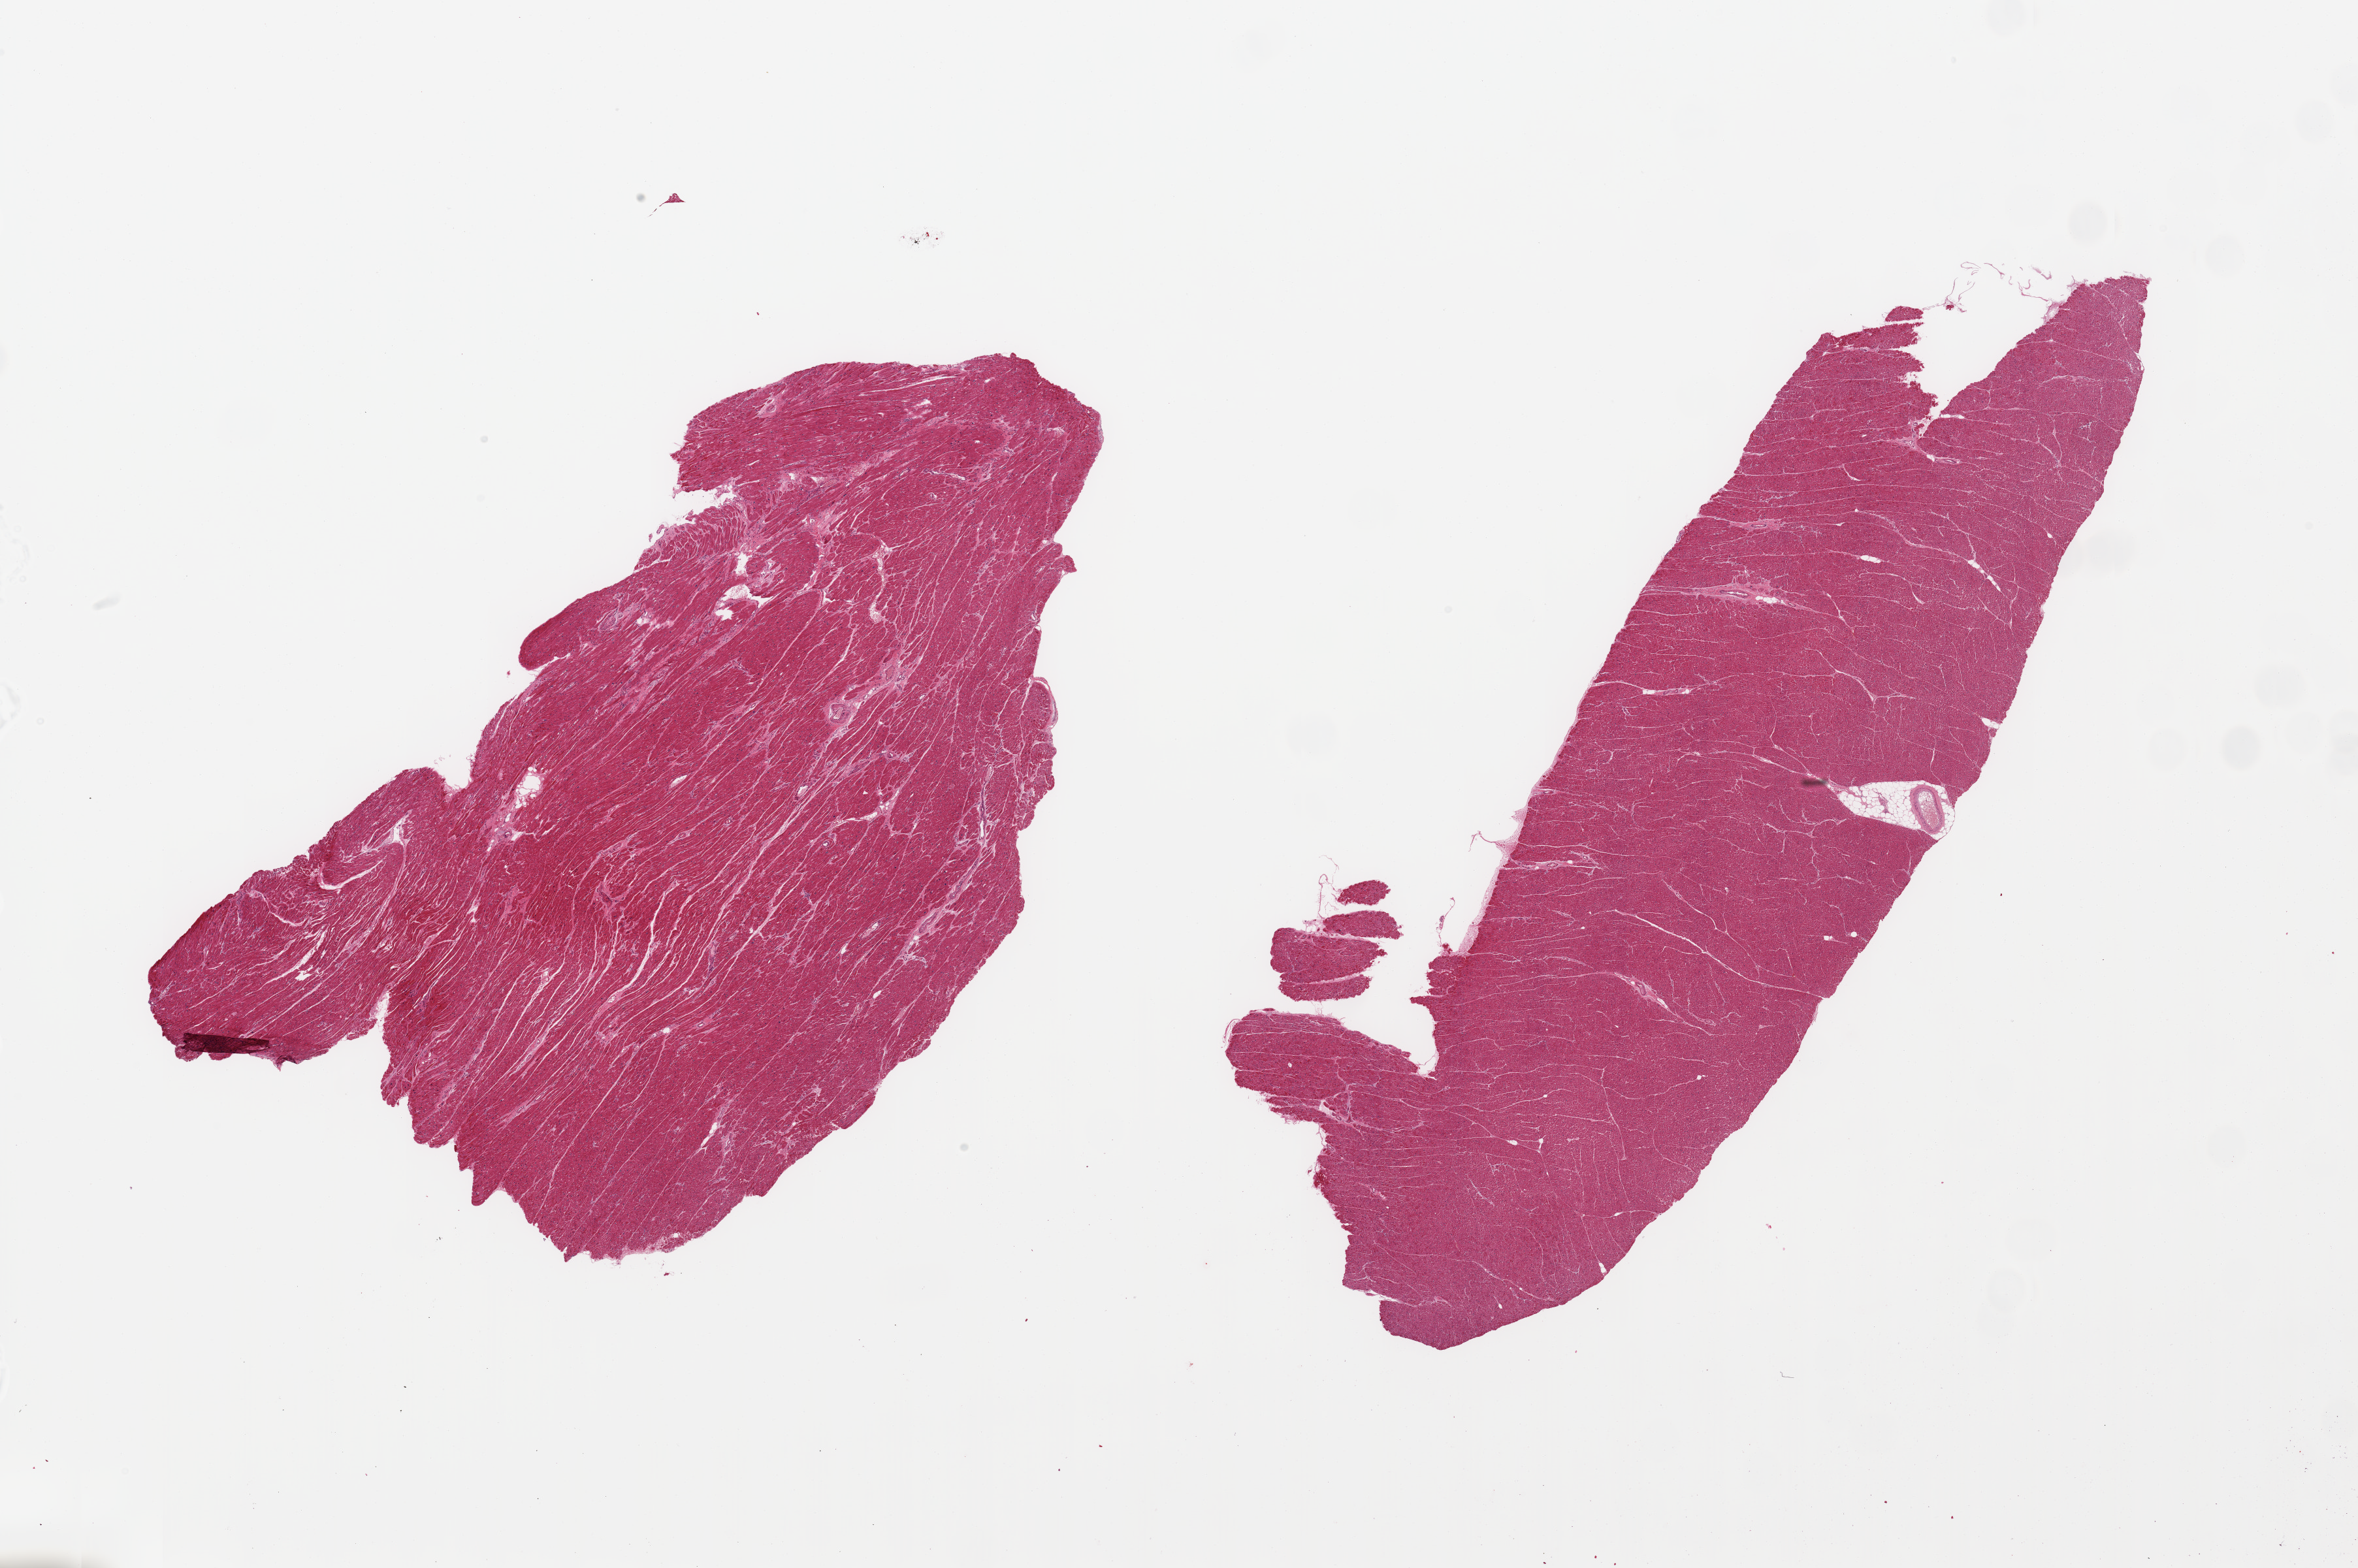
Digitized haematoxylin and eosin-stained section — whole scanned area (about 28.5 x 19.0 mm) shown as a low-resolution overview. PAXgene-fixed paraffin-embedded (PFPE) section. Sampled site (target tissue): heart. Donor tissue sample. Donor sex: male.
* reviewer comment on this tissue sample: 2 pieces; no lesions; <2% fat content